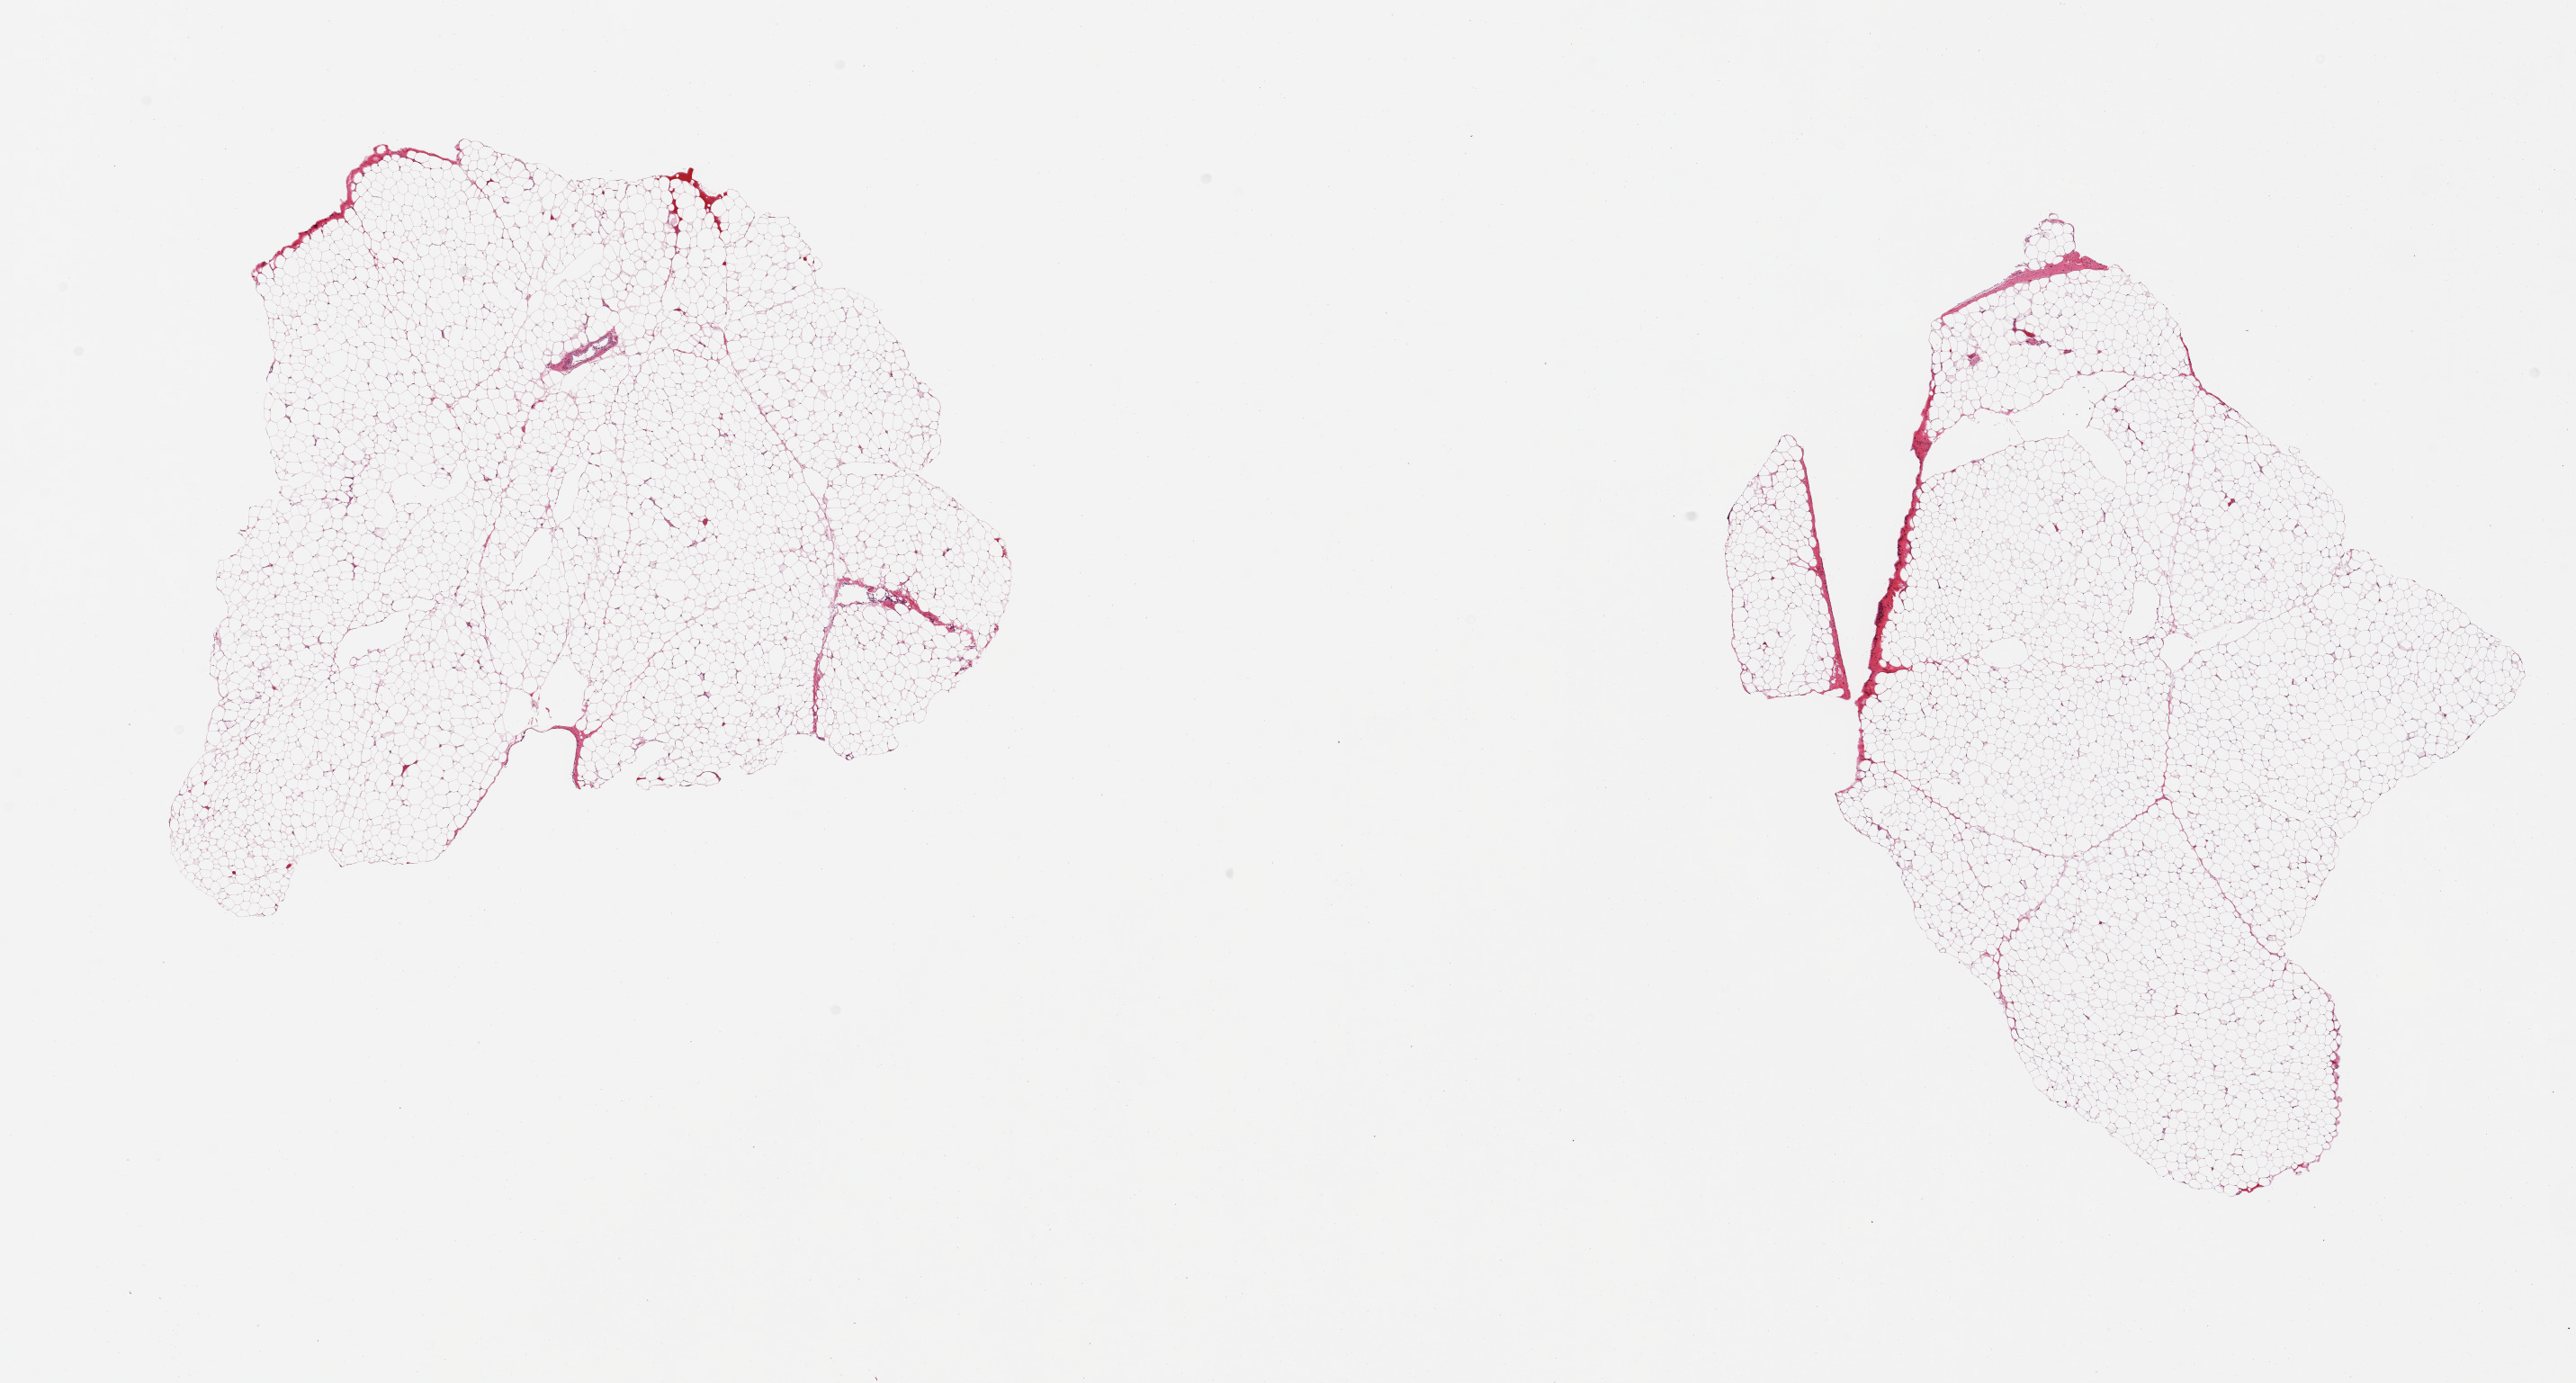
Digitized H&E-stained section — a low-resolution overview of the entire scanned area, about 22.6 x 12.2 mm, PAXgene-fixed, paraffin-embedded tissue, target tissue: omentum, tissue donor sample. Donor sex: male.
- pathologist's review note for this sample: 2 pieces, minimal fascia/vascular elements